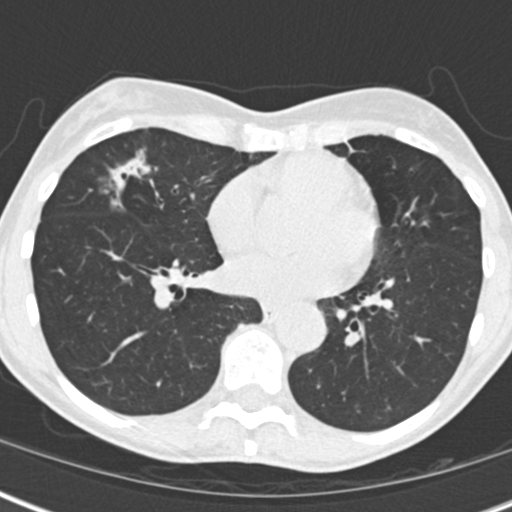
Low-dose screening chest CT, one axial slice; slice 73 of 173 in the series (ordered by position); reconstruction kernel B30f; 120 kVp; lung window (W 1500 / L -600 HU); 512 × 512 image matrix, field of view 290 × 290 mm.
Outlined on this slice (manually delineated by an expert):
- lesion 1 (tumor, middle lobe of right lung): bounding box (x1, y1, x2, y2) in pixels: (112, 157, 150, 187)